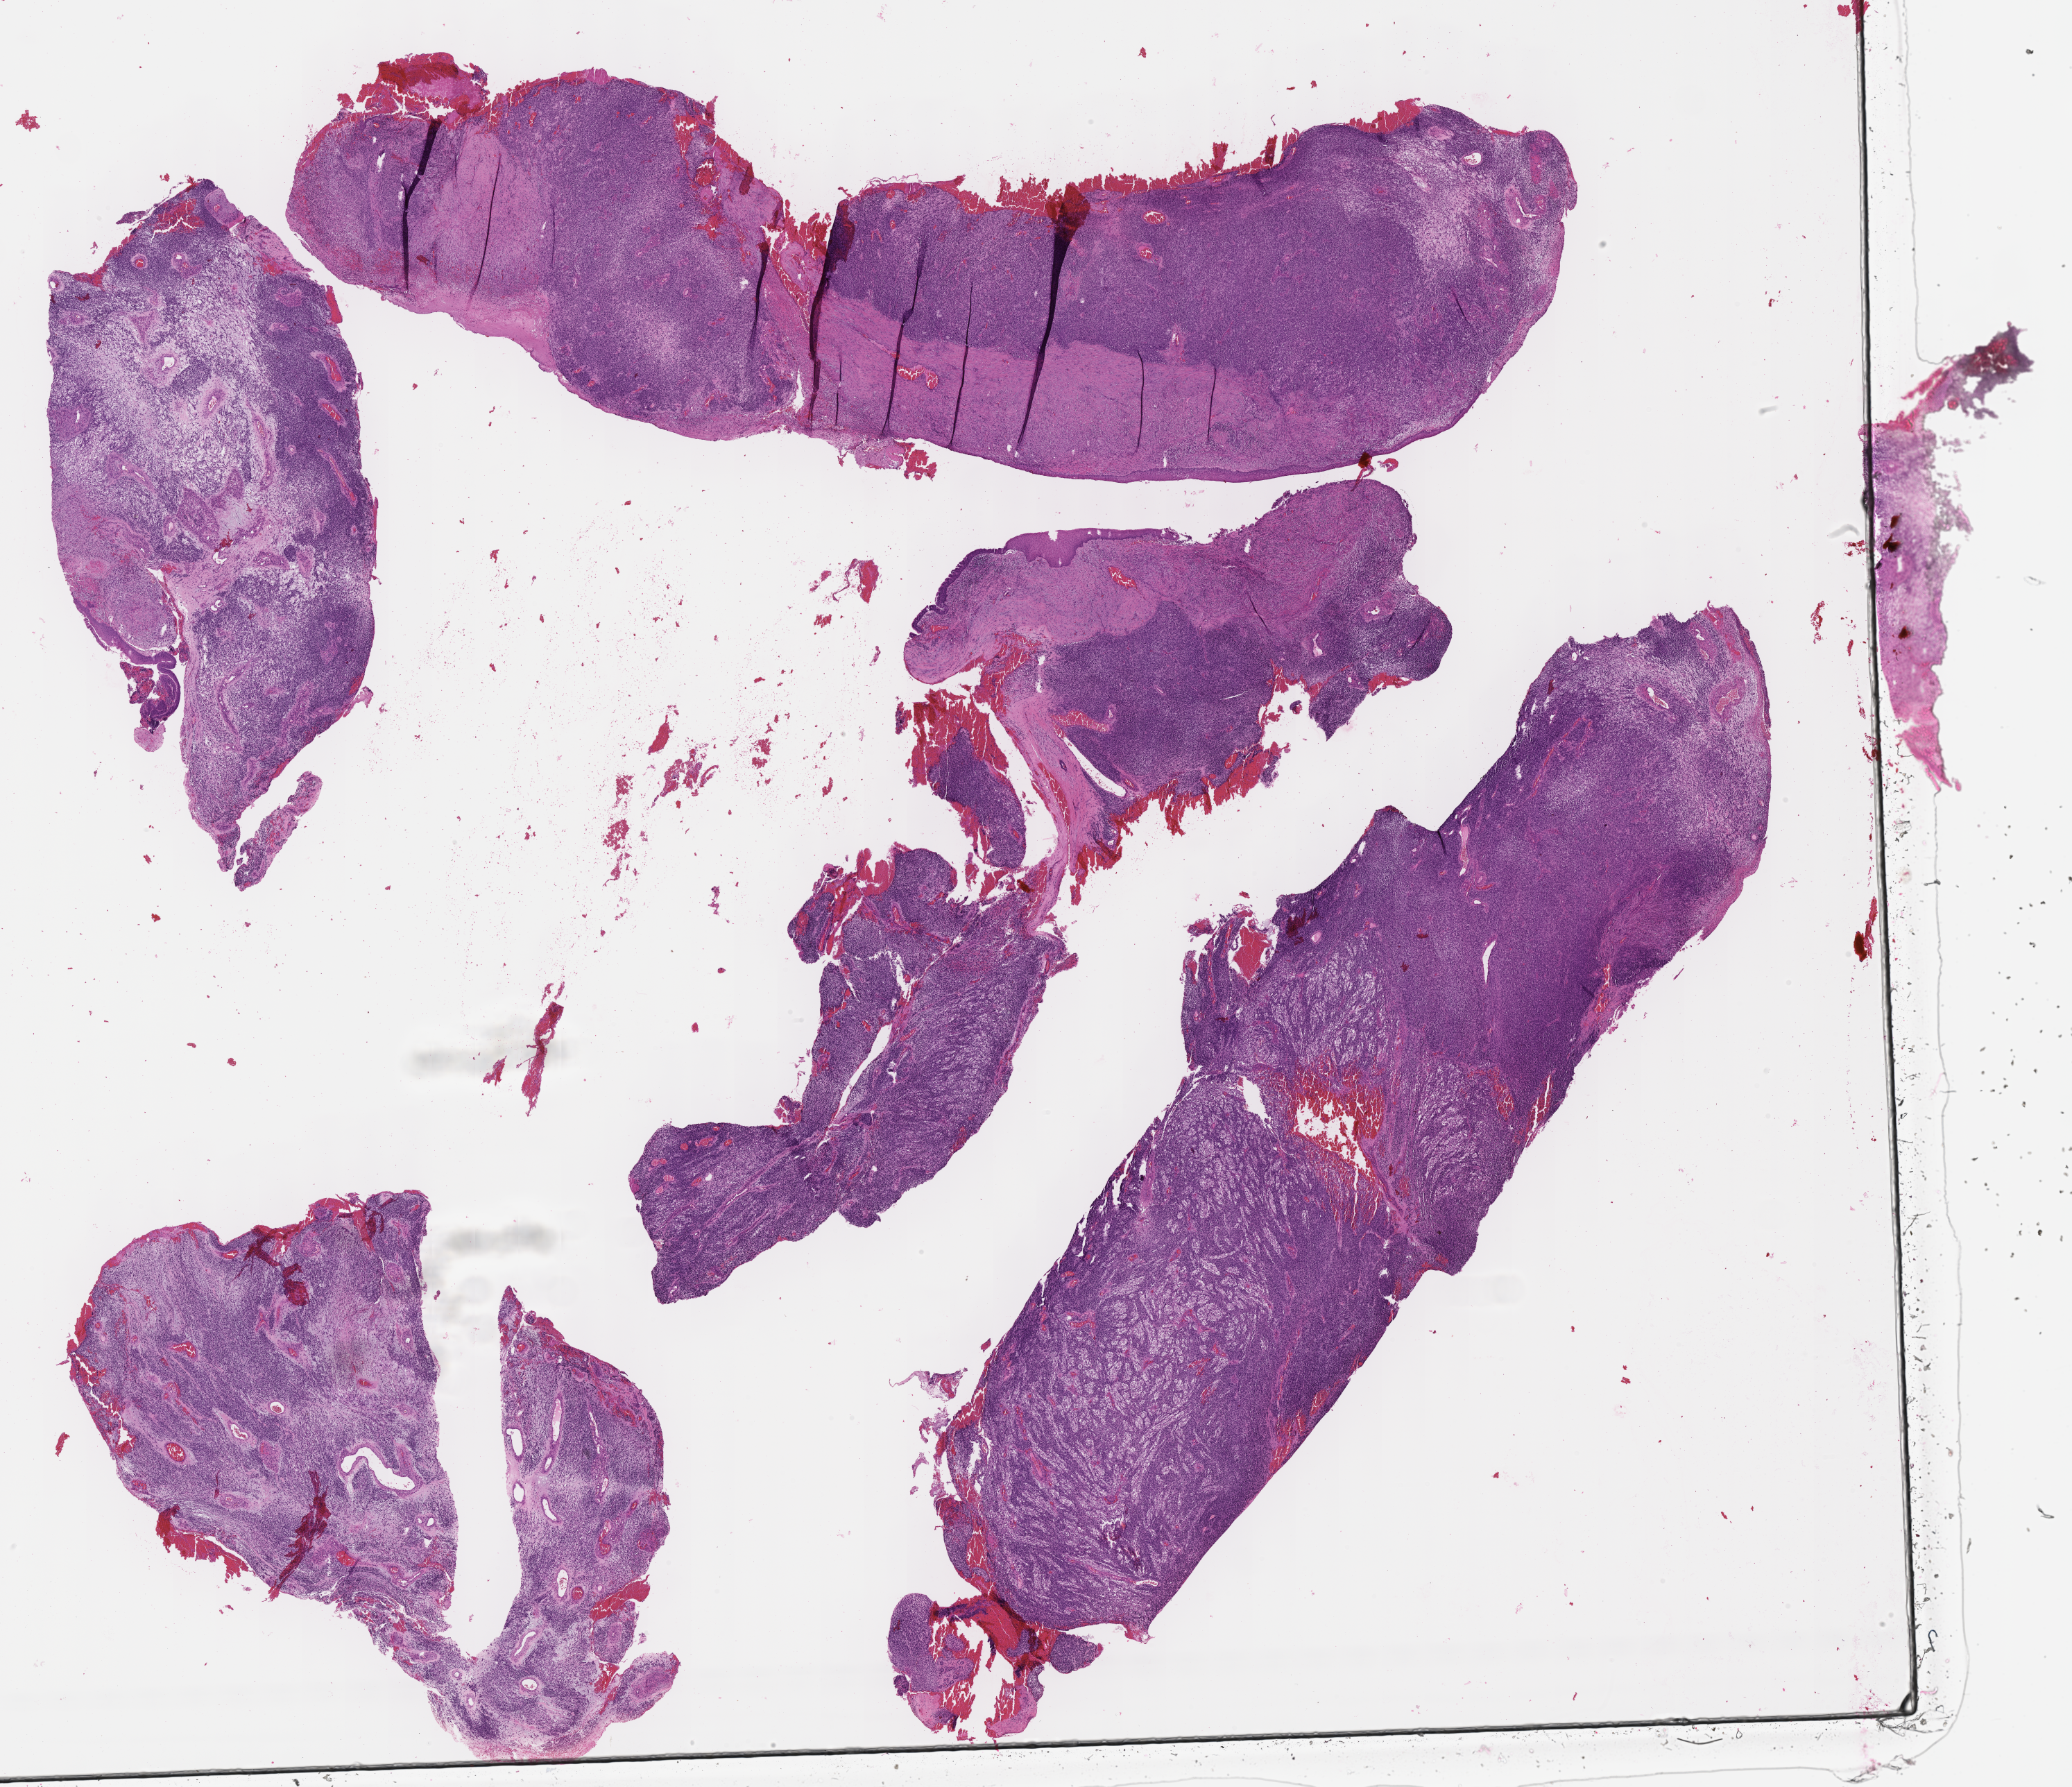
Digitized hematoxylin and eosin (H&E)-stained section of tumor tissue — a low-resolution overview of the entire scanned area, about 24.2 x 20.8 mm, formalin-fixed, paraffin-embedded (FFPE) tissue. Male patient, age at diagnosis 11.5 years.
Metastatic status at presentation (as recorded): non-metastatic. Diagnosis: rhabdomyosarcoma; histological classification: embryonal rhabdomyosarcoma. Stage (as recorded): 2.